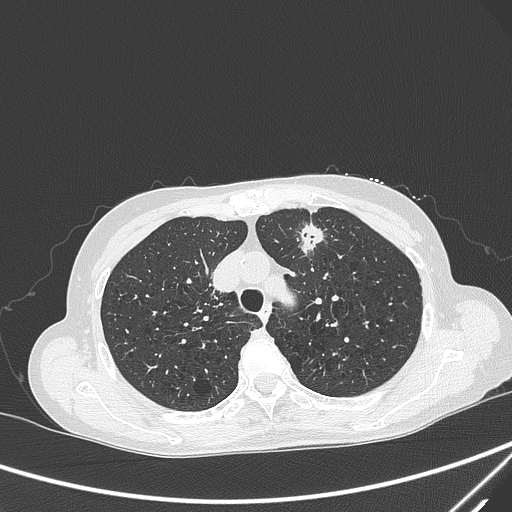
Chest CT, one axial slice. Slice 229 of 299 in the series (ordered by position). 120 kVp. Lung window (W 1500 / L -600 HU). 1 mm slice thickness. 512 × 512 image matrix, field of view 350 × 350 mm. Female patient, age 71 years. From the clinical record (not read from this slice): clinical TNM (as recorded): T1c N0 M0; histopathological grade: G2-3.
Structures marked on this image (bounding box drawn by a radiologist):
- lung tumour (recorded histology: adenocarcinoma): bounding box (x1, y1, x2, y2) in pixels: (295, 218, 325, 262)